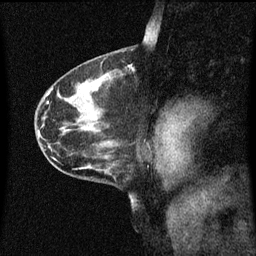
Breast MRI (dynamic contrast-enhanced), one sagittal slice; dynamic contrast-enhanced series, image 2 of 3 at this slice position (ordered by acquisition); 1.5 T; TE 4.2 ms, TR 8.4 ms; 256 × 256 image matrix. Patient: female, 41 years.
Structures marked on this image (semi-automatic segmentation, software-assisted and operator-edited):
- analysis volume of interest (the breast-tissue region the enhancement analysis was run in; not a lesion): box from (x=121, y=58) to (x=141, y=83) px
- tumour enhancement mask (voxels above the 70 % enhancement threshold inside the analysis volume of interest): (x=126, y=66)–(x=135, y=73)